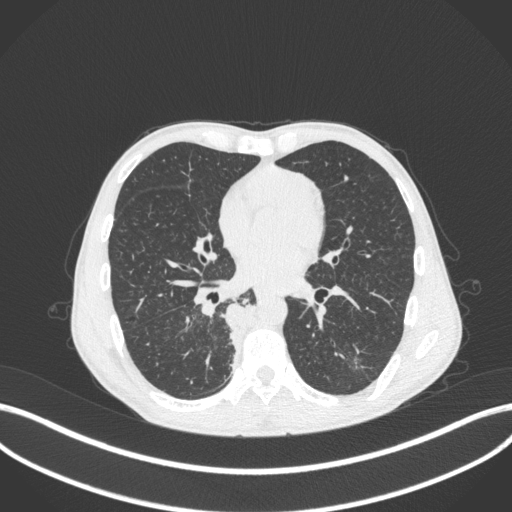
Chest CT, one axial slice; position 176 of 371 along the scan axis; reconstruction kernel B31f; 120 kVp; lung window (W 1500 / L -600 HU); 1 mm slice thickness; 512 × 512 image matrix. Patient: male, 58 years. From the clinical record (not read from this slice): clinical TNM (as recorded): T3 N1 M1.
Annotated regions visible in this slice (rectangle marked by the reading radiologist):
- lung tumour (recorded histology: squamous cell carcinoma): bounding box (x1, y1, x2, y2) in pixels: (225, 304, 258, 364)